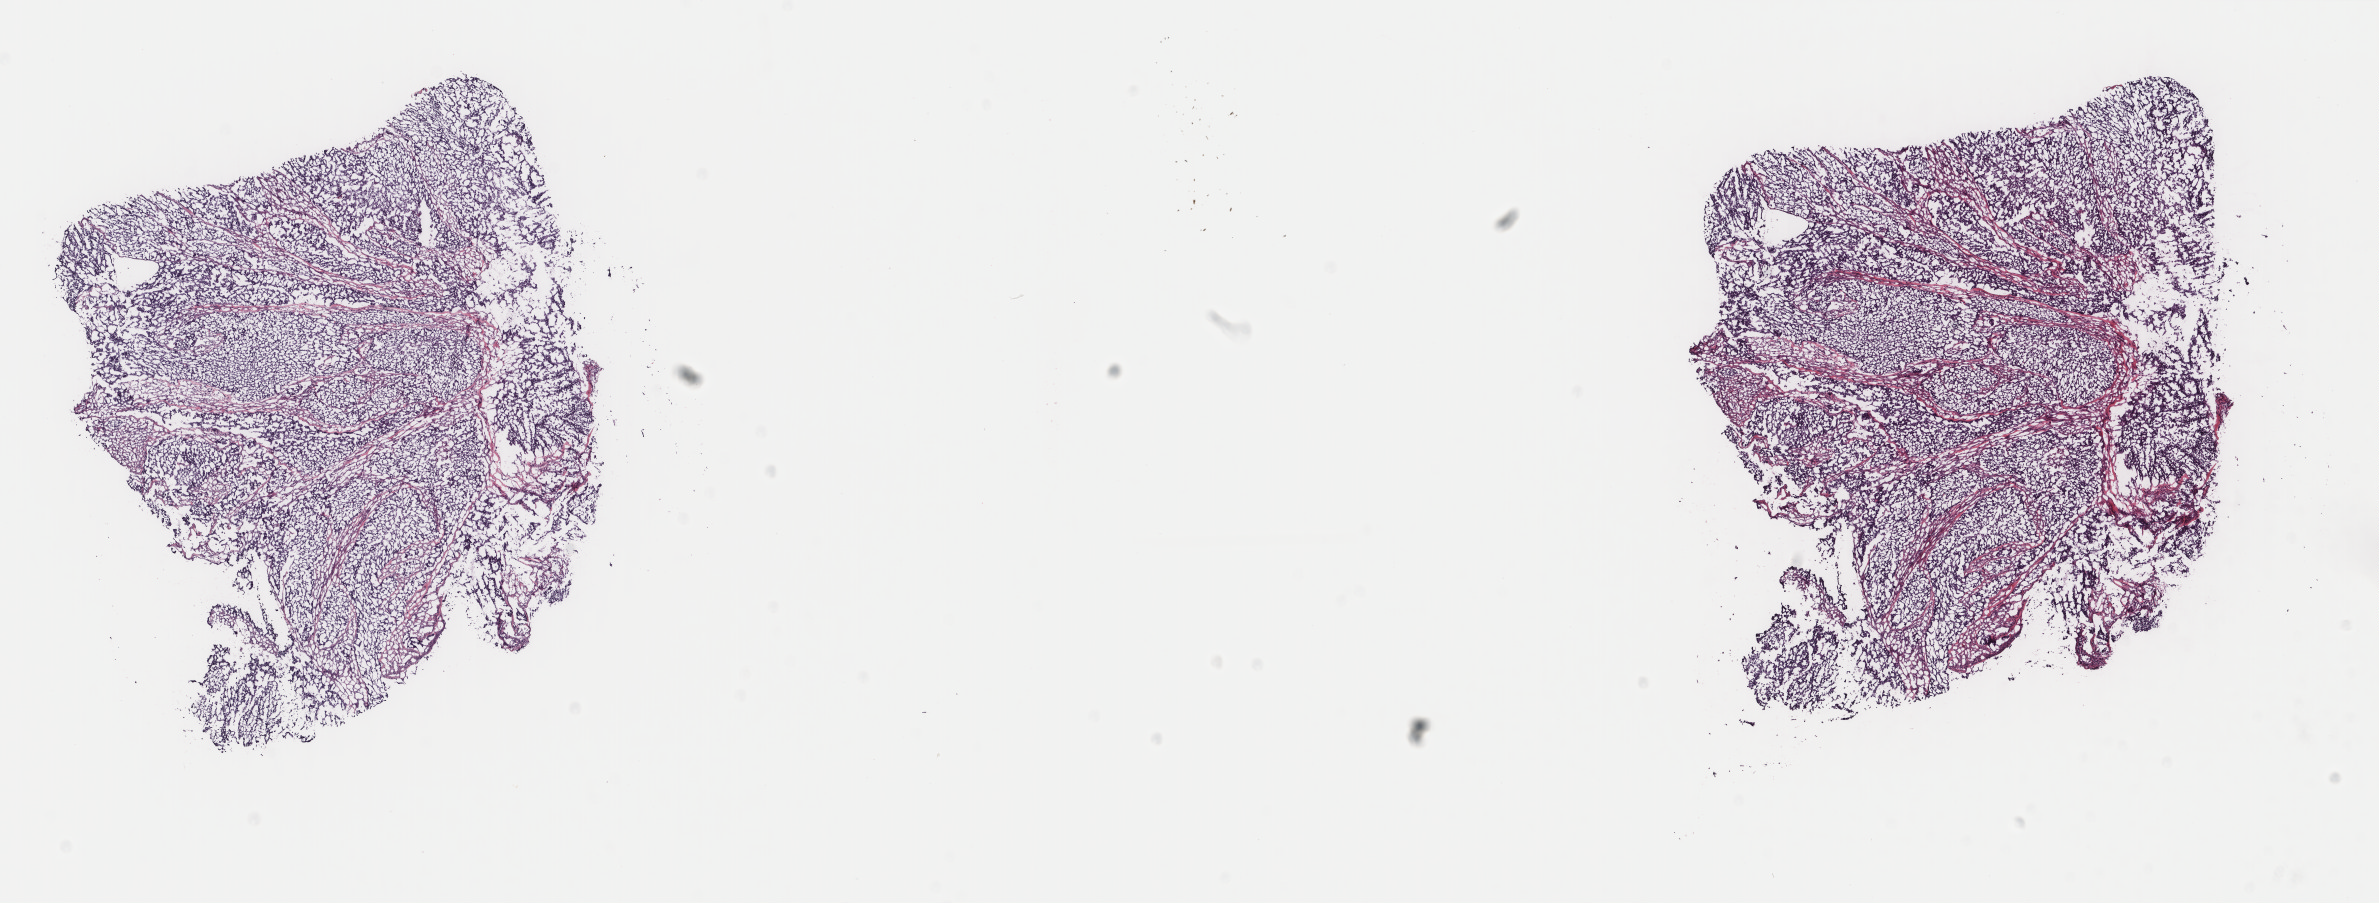
Hematoxylin and eosin (H&E) stained whole-slide image — a low-resolution overview of the entire scanned area, about 18.9 x 7.2 mm (from a 40x scan); frozen section from the top of the tissue portion; primary tumour sample from the bladder. Male patient. Histologic grade: high grade. Slide review estimates, as recorded: tumour cells 85%, tumour nuclei 85%, normal cells 0%, stromal cells 15%, necrosis 0%. Infiltration values recorded for this section: lymphocyte infiltration 2%, monocyte infiltration 0%, neutrophil infiltration 0%.
Histologic diagnosis: Transitional cell carcinoma (anterior wall of bladder). AJCC pathologic stage: III. Lymph nodes positive (case pathology): 0 of 26 examined.